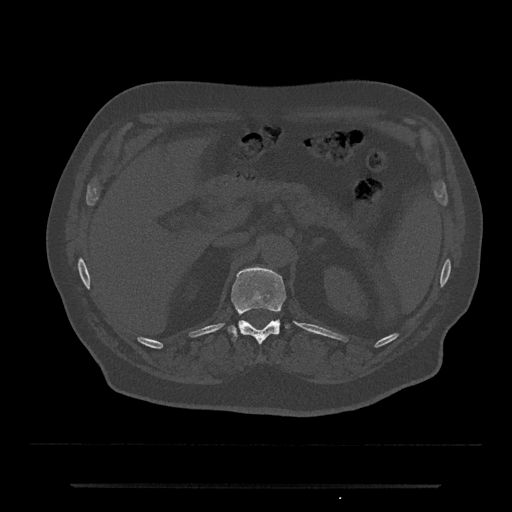
CT including the spine, one axial slice. Slice 589 of 797 in the series (ordered by position). Reconstruction kernel Br40s/3. 120 kVp. Bone window (W 1800 / L 400 HU). 0.5 mm slice thickness. 512 × 512 image matrix, field of view 434 × 434 mm. Patient: male, 80 years. Case-level facts recorded for this patient, not image findings: primary cancer: prostate; vertebrae with lytic lesions (as recorded): L1, T11.
Outlined on this slice (semi-automatic segmentation, software-assisted and operator-edited):
- T12 vertebra: bounding box [x1, y1, x2, y2] px = [228, 267, 288, 345]